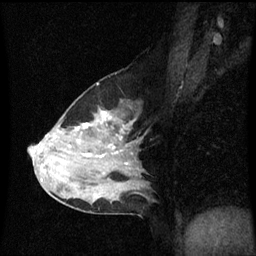
Breast MRI (dynamic contrast-enhanced), one sagittal slice; position 37 of 60 along the scan axis; dynamic contrast-enhanced series, image 2 of 3 at this slice position (ordered by acquisition); 1.5 T; TE 4.2 ms, TR 8.9 ms; 2 mm slice thickness; 256 × 256 image matrix, field of view 200 × 200 mm. Patient: female, 50 years. From the clinical record (not read from this slice): setting: breast cancer imaged before/during neoadjuvant chemotherapy; receptor status: HR-positive, HER2-negative.
Structures marked on this image (semi-automatic segmentation, software-assisted and operator-edited):
- analysis volume of interest (the breast-tissue region the enhancement analysis was run in; not a lesion): box from (x=33, y=96) to (x=146, y=209) px
- tumour enhancement mask (voxels above the 70 % enhancement threshold inside the analysis volume of interest): (x=84, y=112)–(x=119, y=153)